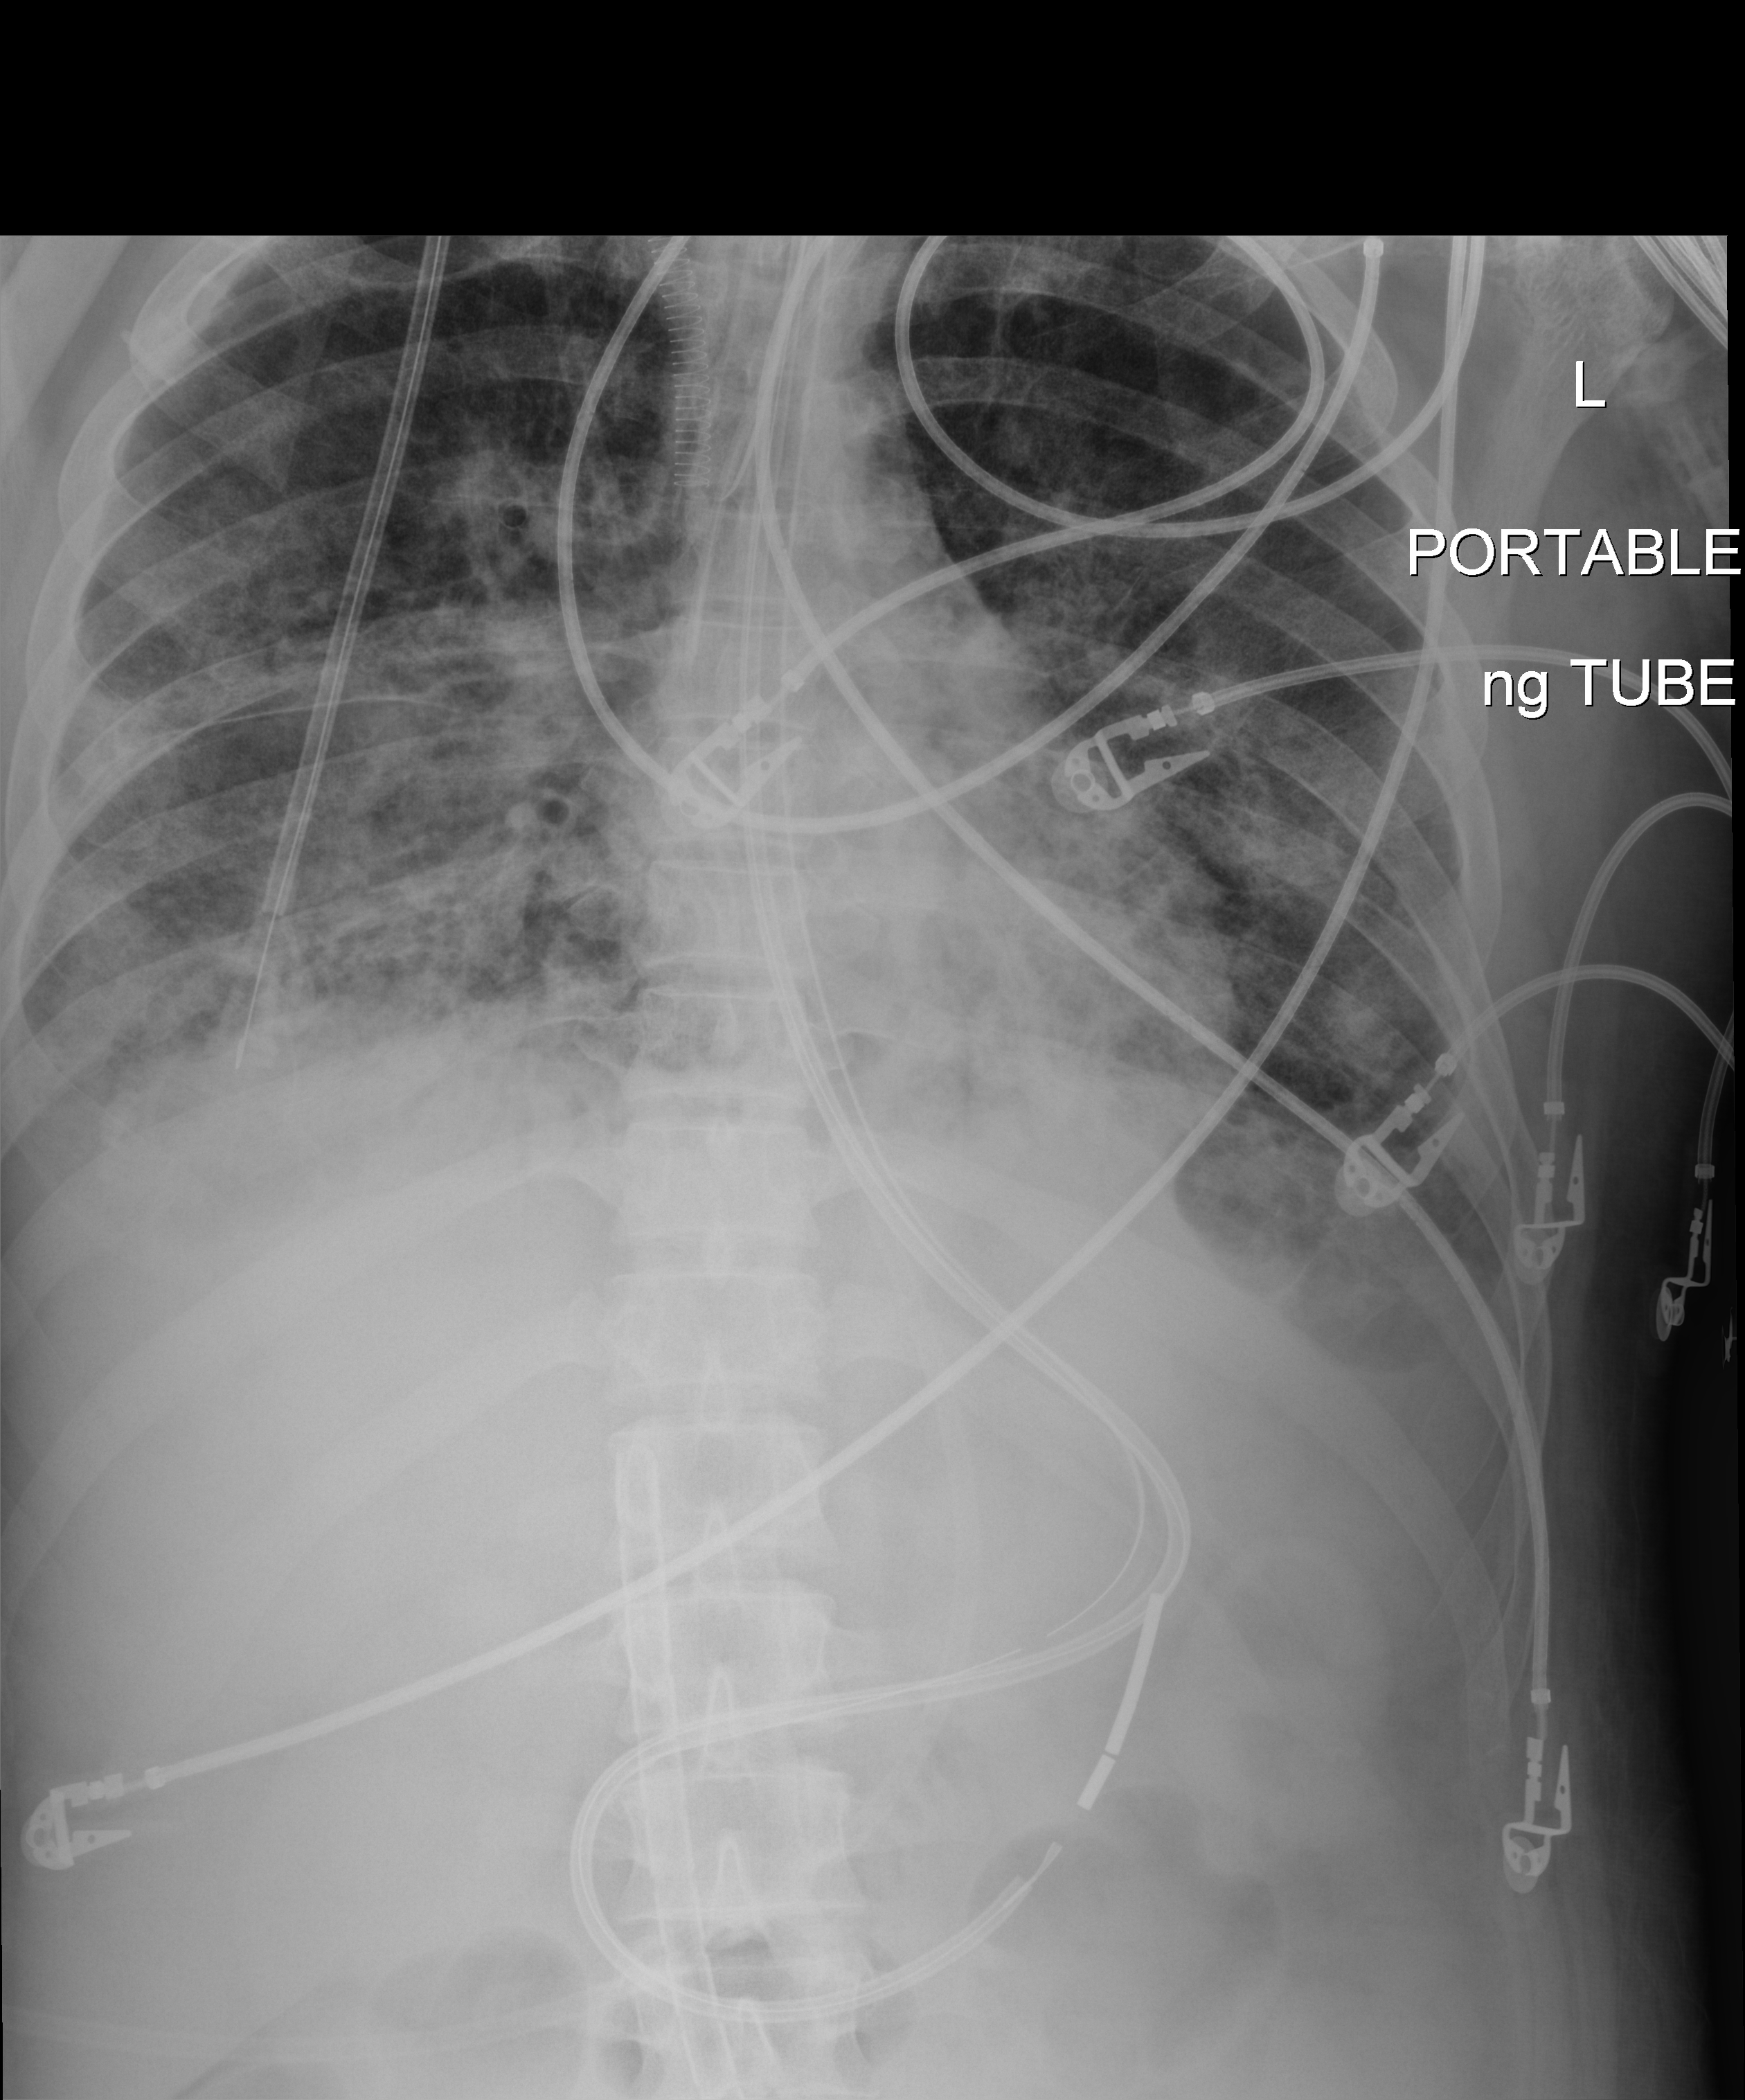
Abdomen X-ray (portable). Adult patient hospitalised with COVID-19, age 18–59 years.
From the hospital-stay record, not from the radiograph (when in the stay this image was taken is not recorded): smoking status (admission record): never.